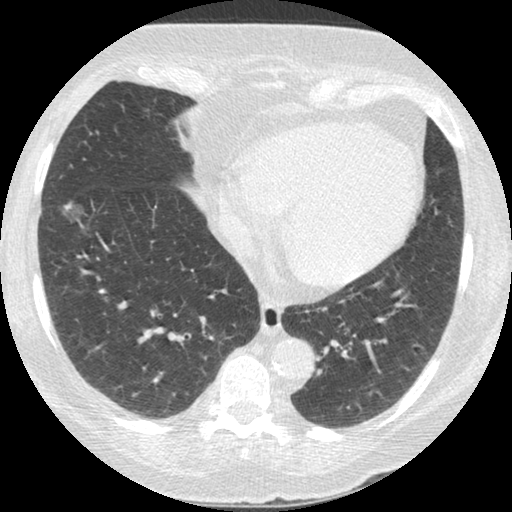
Low-dose screening chest CT, one axial slice; position 95 of 245 along the scan axis; lung window (W 1500 / L -600 HU); 1.25 mm slice thickness; 512 × 512 image matrix, field of view 310 × 310 mm.
Structures marked on this image (expert manual segmentation):
- lesion 1 (tumor, lower lobe of right lung): bounding box [x1, y1, x2, y2] px = [62, 202, 83, 220]